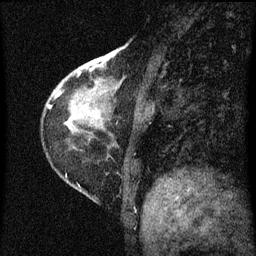
Breast MRI (dynamic contrast-enhanced), one sagittal slice; slice 19 of 60 in the series (ordered by position); dynamic contrast-enhanced series, image 2 of 3 at this slice position (ordered by acquisition); 1.5 T; TE 4.2 ms, TR 8 ms; 256 × 256 image matrix, field of view 180 × 180 mm. Patient: female, 38 years.
Outlined on this slice (semi-automatic segmentation, software-assisted and operator-edited):
- analysis volume of interest (the breast-tissue region the enhancement analysis was run in; not a lesion): bounding box <67,46,140,131> (left, top, right, bottom; pixels)
- tumour enhancement mask (voxels above the 70 % enhancement threshold inside the analysis volume of interest): <78,60,103,117>